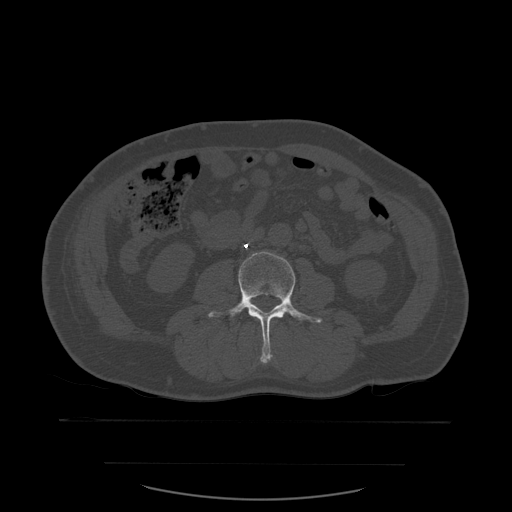
CT including the spine, one axial slice; position 192 of 590 along the scan axis; bone window (W 1800 / L 400 HU); 1.25 mm slice thickness; 512 × 512 image matrix, field of view 479 × 479 mm. Patient age 71 years. From the clinical record (not read from this slice): primary cancer: lung.
Annotated regions visible in this slice (semi-automatically segmented with operator editing):
- L3 vertebra: bounding box (x1, y1, x2, y2) in pixels: (208, 252, 323, 364)